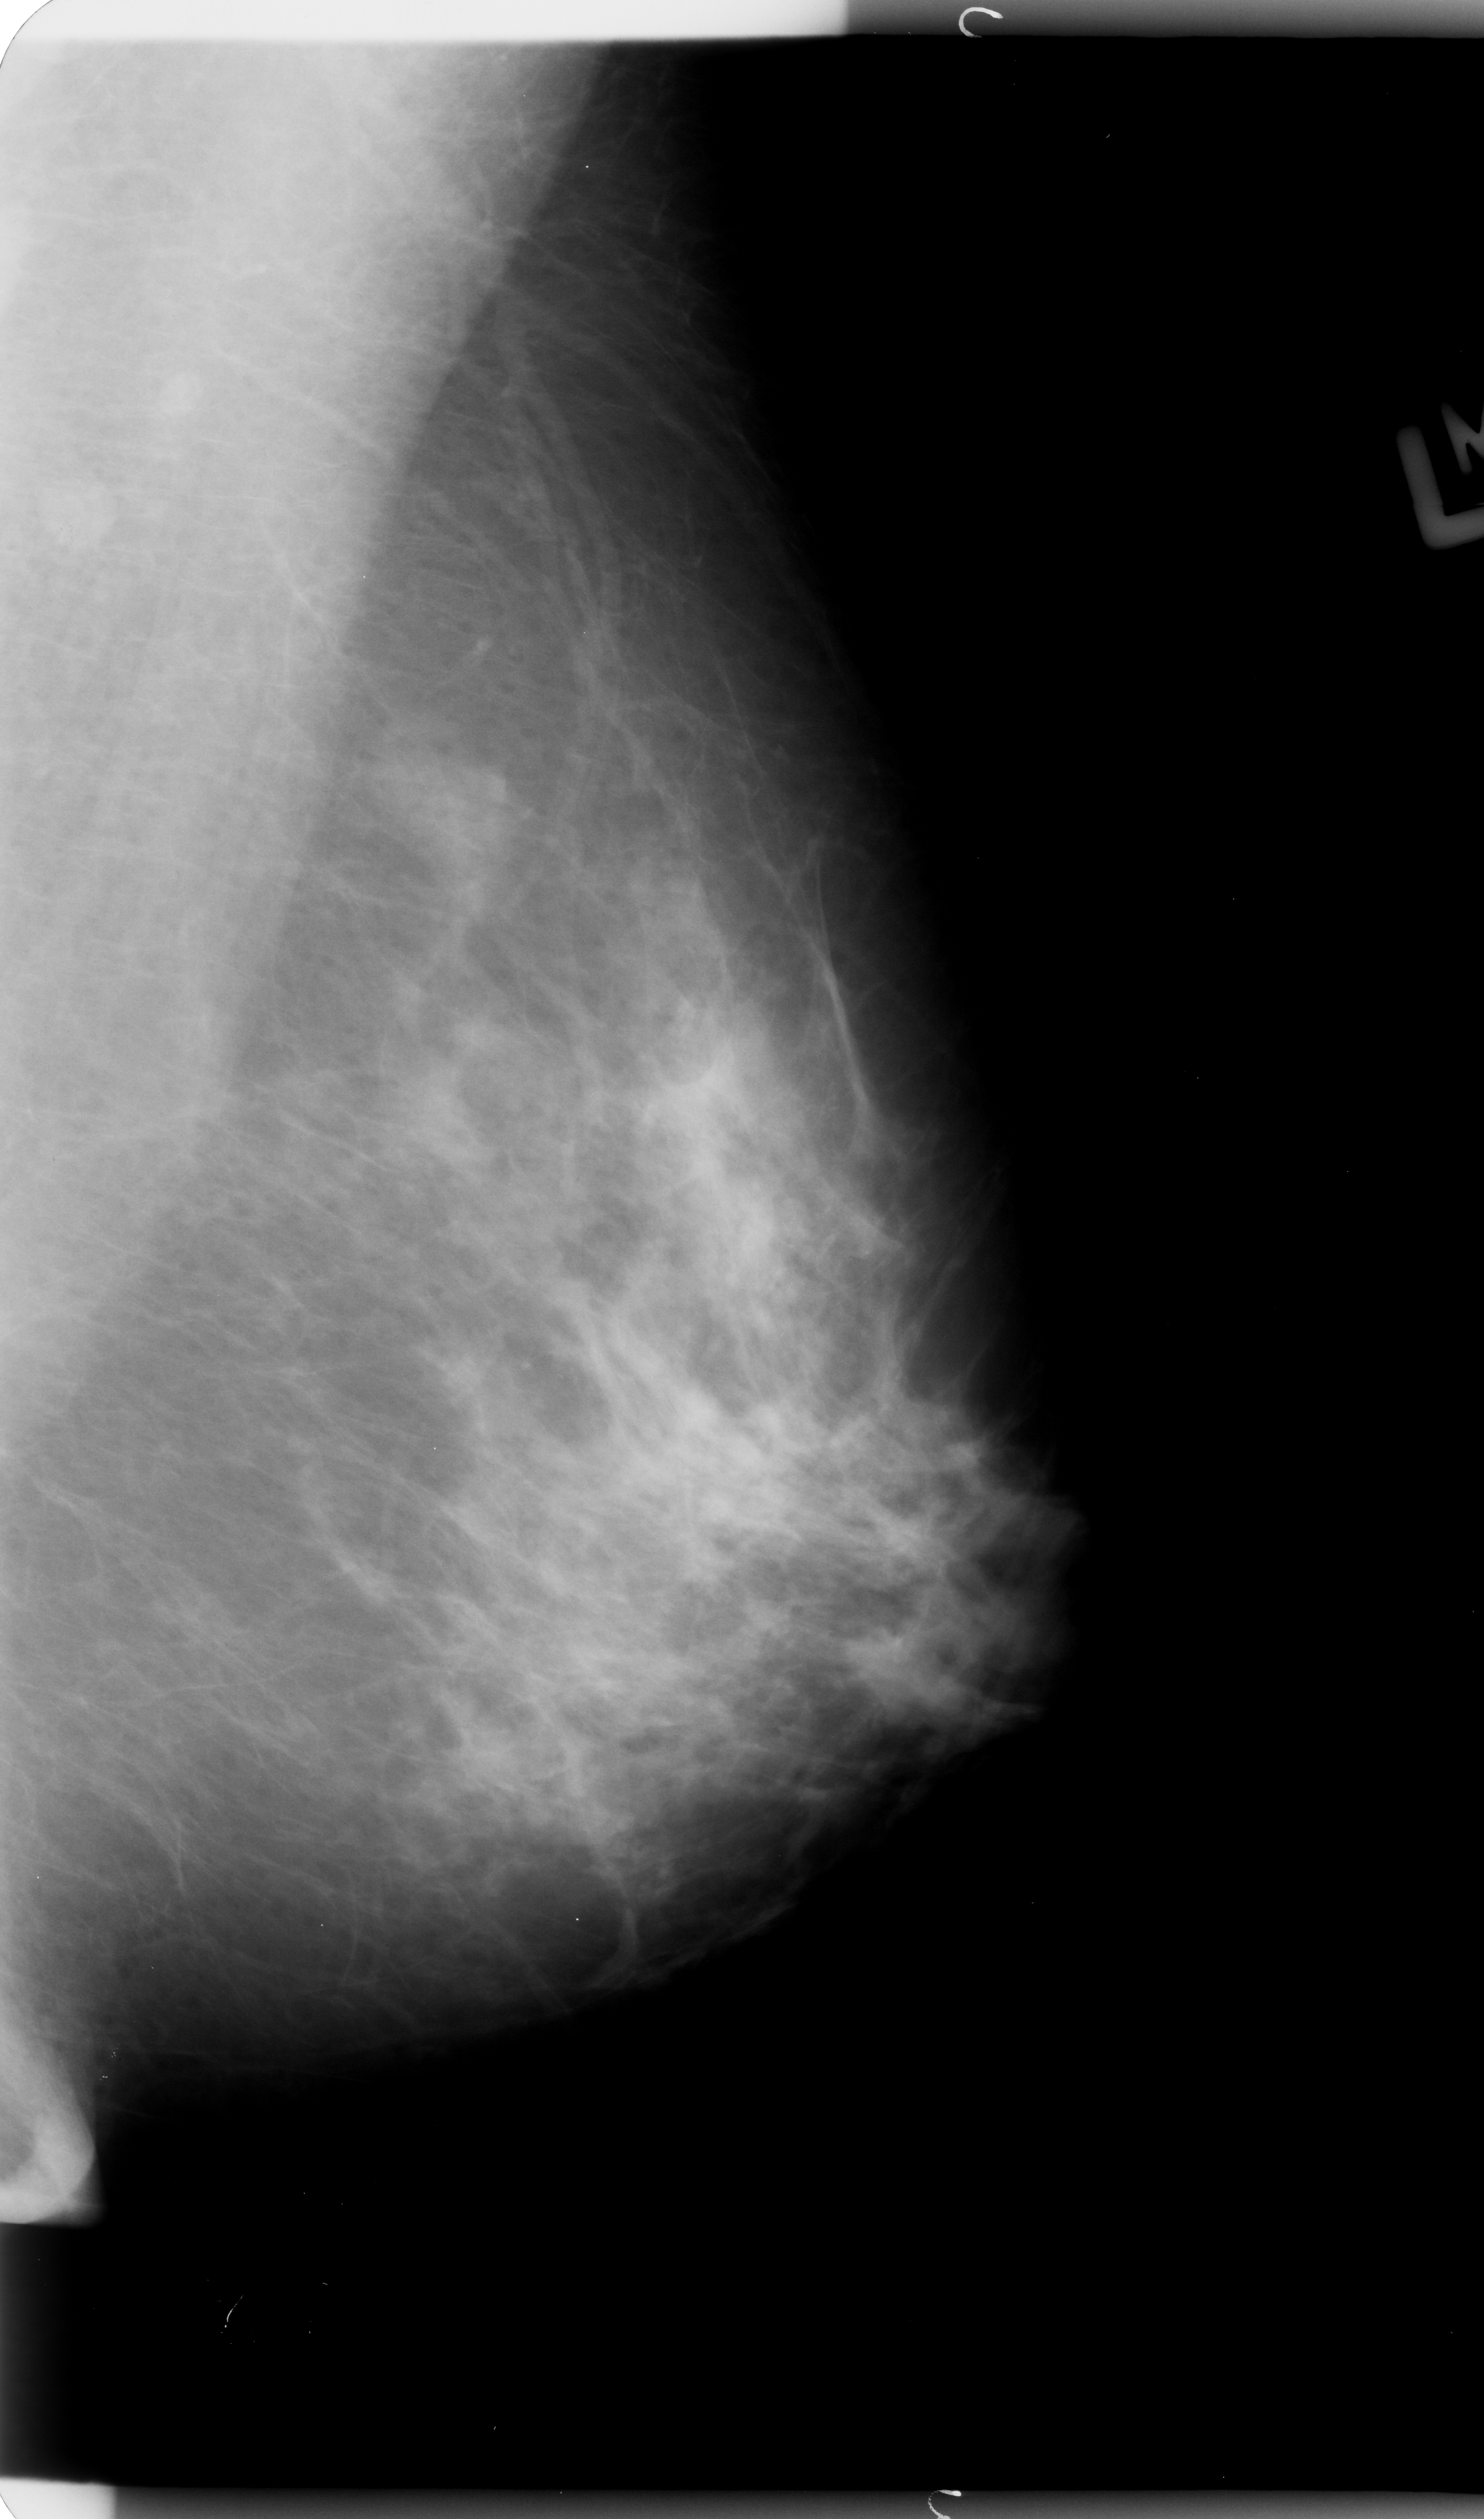
Mammogram (digitized film); left breast; MLO view; BI-RADS breast density category 3 (scale 1–4).
- Marked abnormality: mass, shape irregular, margins ill defined; BI-RADS assessment category 3; subtlety rating 3 on a 1 (subtle) to 5 (obvious) scale; pathology (as recorded): benign.